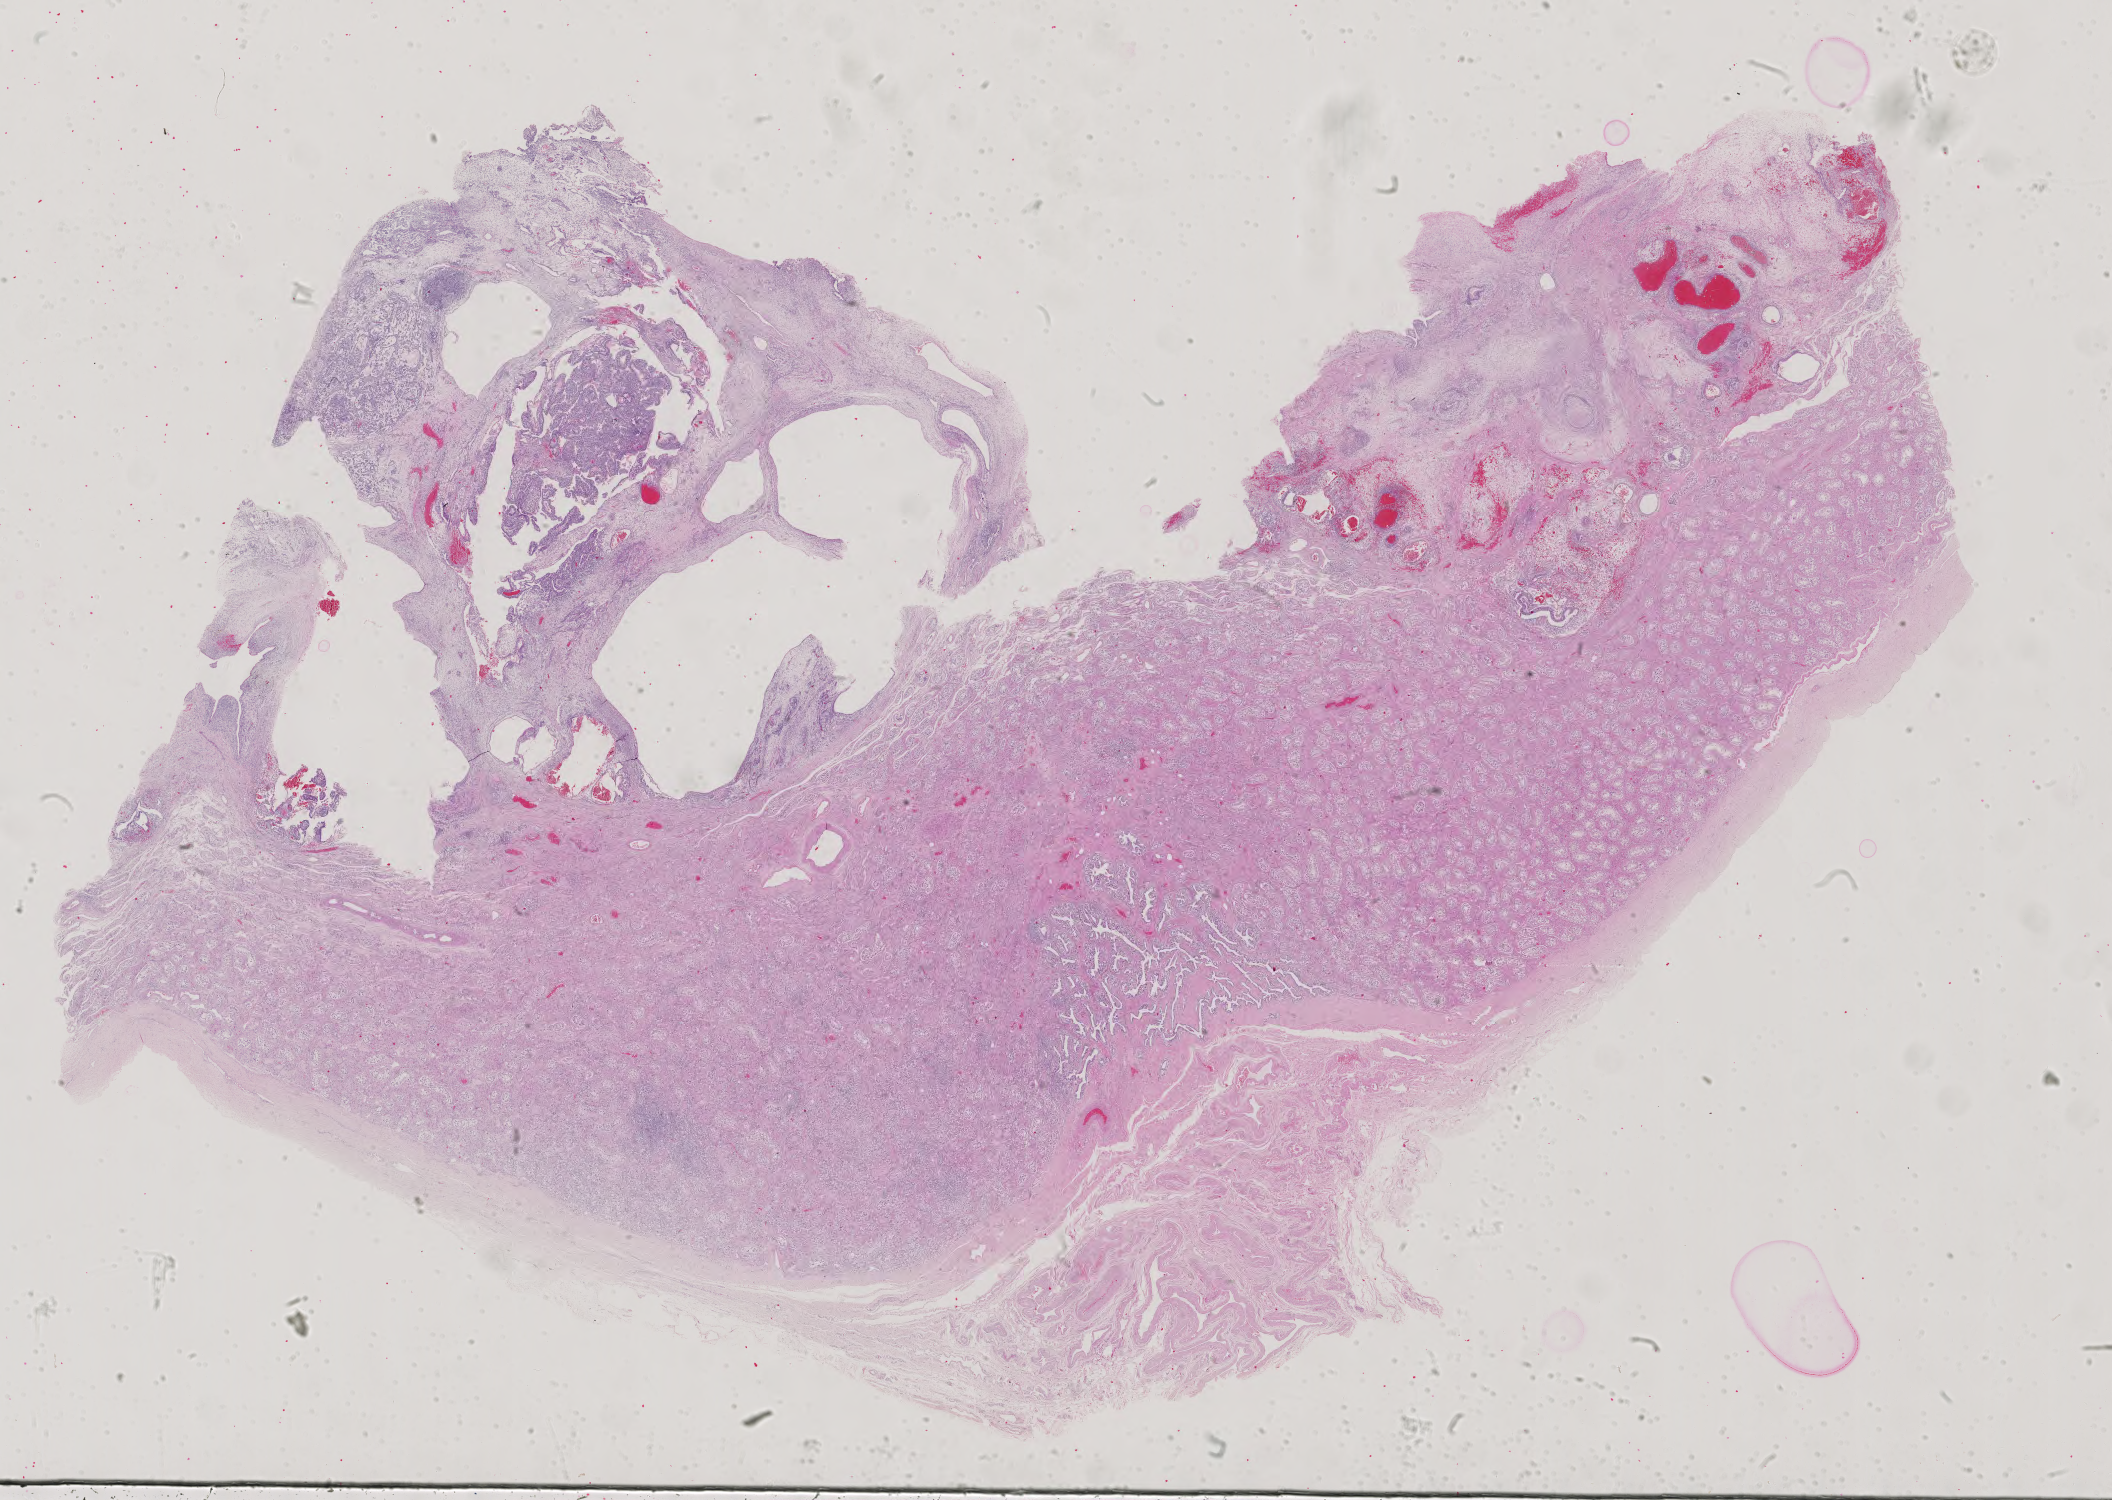
Whole-slide histology image, Hematoxylin and eosin (H&E) stained, whole scanned area (about 30.8 x 21.9 mm) shown as a low-resolution overview, FFPE section, testis, primary tumour sample. Male, age 33 years at initial diagnosis.
- TNM: T1 N0 M0
- AJCC pathologic stage: IS (6th edition)
- diagnosis: Mixed germ cell tumor